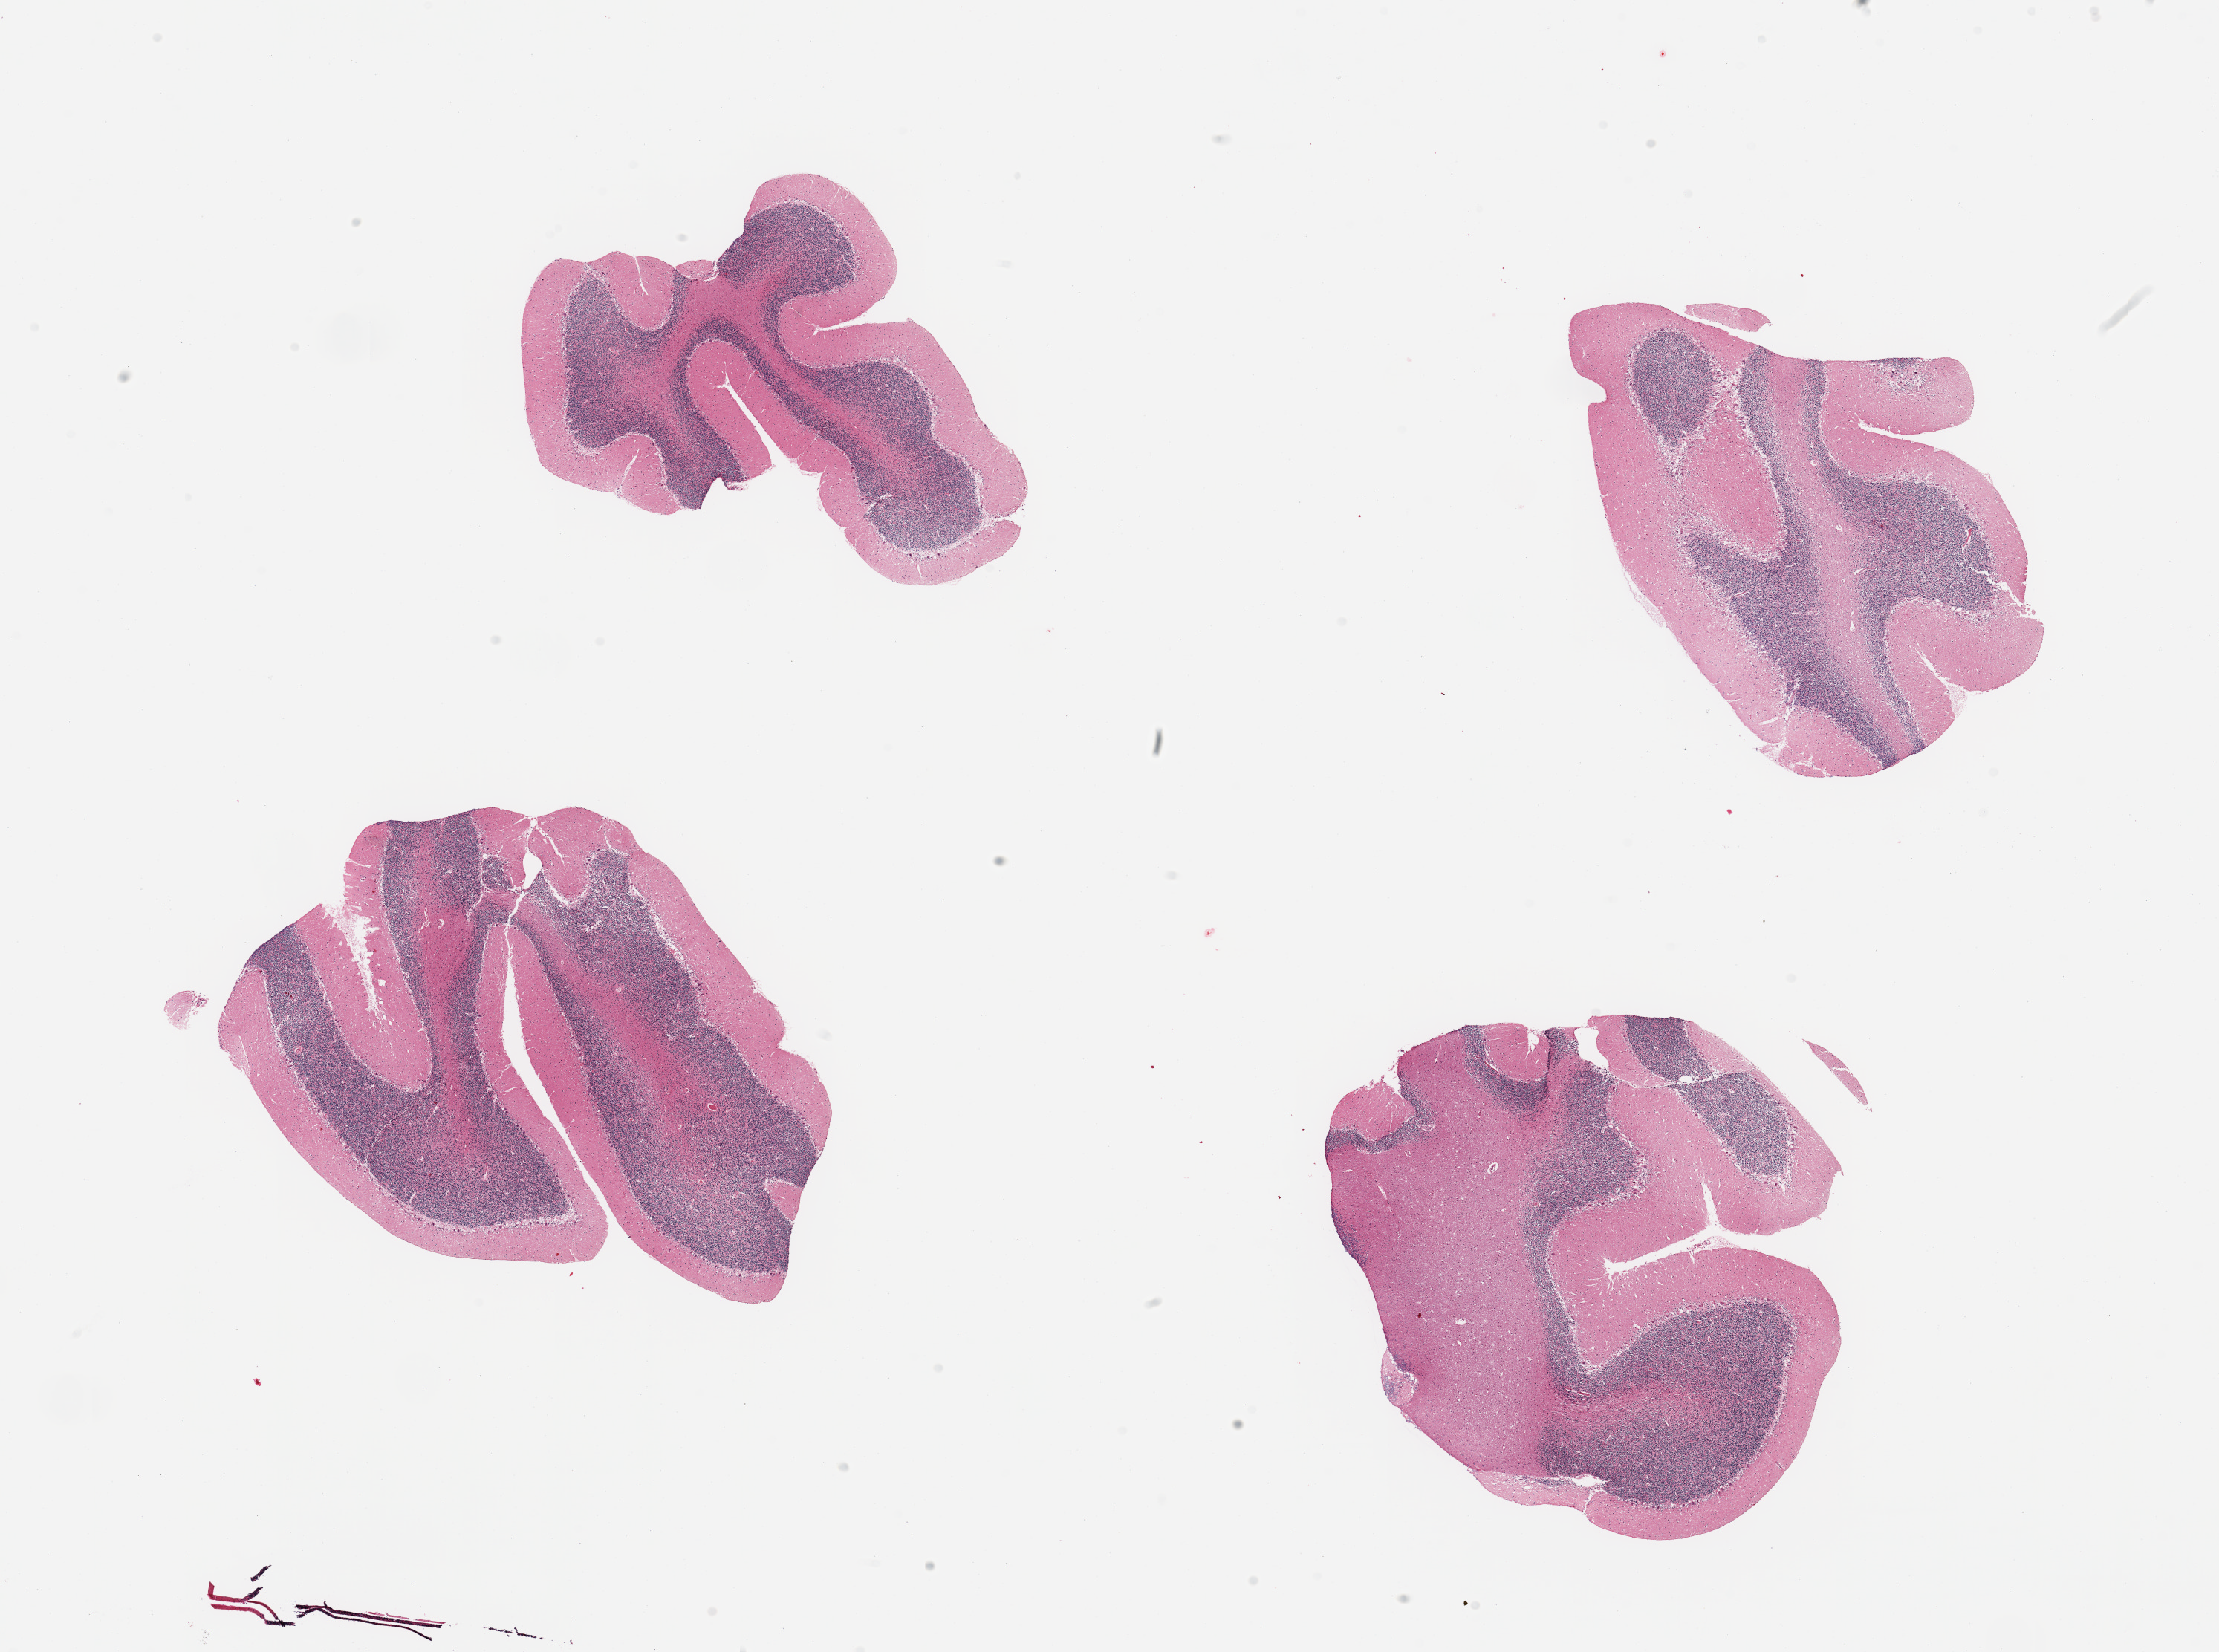
H&E whole-slide image — a low-resolution overview of the entire scanned area, about 23.6 x 17.6 mm. PAXgene-fixed, paraffin-embedded tissue. Section of cerebellum (target tissue). Tissue donor sample. Donor sex: male.
Reviewer comment on this tissue sample: 4 pieces.